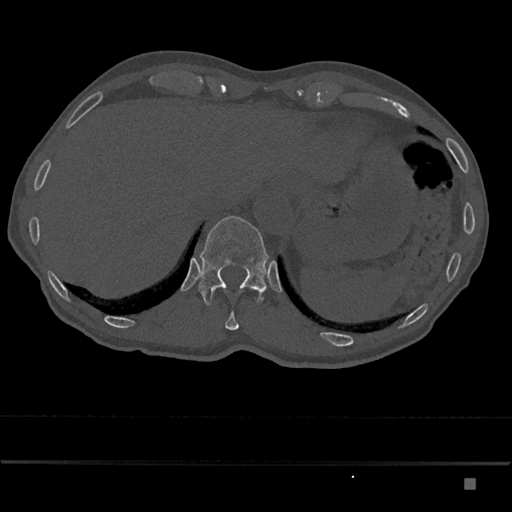
CT including the spine, one axial slice; position 633 of 797 along the scan axis; reconstruction kernel Br40s/3; 120 kVp; bone window (W 1800 / L 400 HU); 0.5 mm slice thickness; 512 × 512 image matrix. Male patient, age 72 years. From the clinical record (not read from this slice): primary cancer: prostate.
Outlined on this slice (semi-automatic segmentation, software-assisted and operator-edited):
- T11 vertebra: box from (x=225, y=312) to (x=239, y=330) px
- T12 vertebra: (x=198, y=216)–(x=269, y=305)